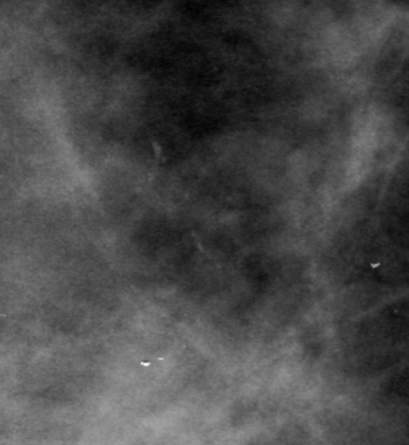
Cropped region of a digitized screen-film mammogram centred on a radiologist-marked abnormality; right breast; CC view.
Calcifications, morphology punctate, distribution clustered; BI-RADS assessment category 0 (incomplete: needs additional imaging); pathology (as recorded): malignant.